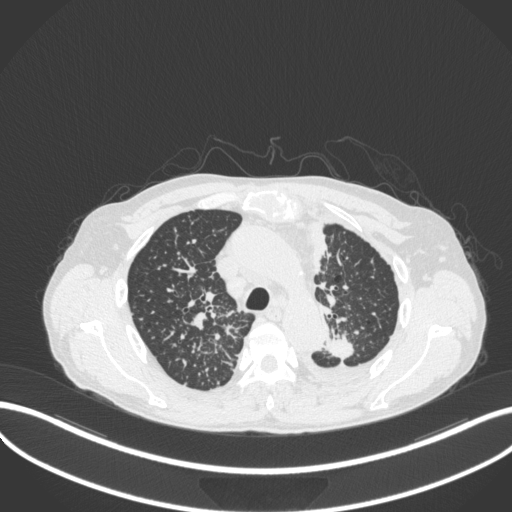
Chest CT, one axial slice. Position 259 of 319 along the scan axis. Reconstruction kernel B31f. Lung window (W 1500 / L -600 HU). 512 × 512 image matrix, field of view 400 × 400 mm. Male patient, age 58 years. Case-level facts recorded for this patient, not image findings: clinical TNM (as recorded): T1c N3 M1.
Annotated regions visible in this slice (rectangle marked by the reading radiologist):
- lung tumour (recorded histology: adenocarcinoma): bounding box (x1, y1, x2, y2) in pixels: (323, 332, 356, 361)